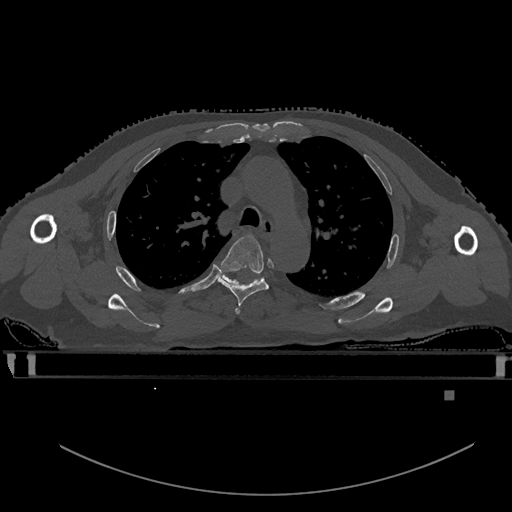
CT including the spine, one axial slice. Slice 399 of 969 in the series (ordered by position). Bone window (W 1800 / L 400 HU). 0.5 mm slice thickness. 512 × 512 image matrix. Male patient, age 82 years. From the clinical record (not read from this slice): primary cancer: prostate; vertebrae with lytic lesions (as recorded): T11, T9, T8, T2.
Structures marked on this image (semi-automatic segmentation, software-assisted and operator-edited):
- T3 vertebra: box from (x=235, y=308) to (x=240, y=314) px
- T4 vertebra: (x=218, y=235)–(x=268, y=308)
- T5 vertebra: (x=217, y=271)–(x=262, y=284)